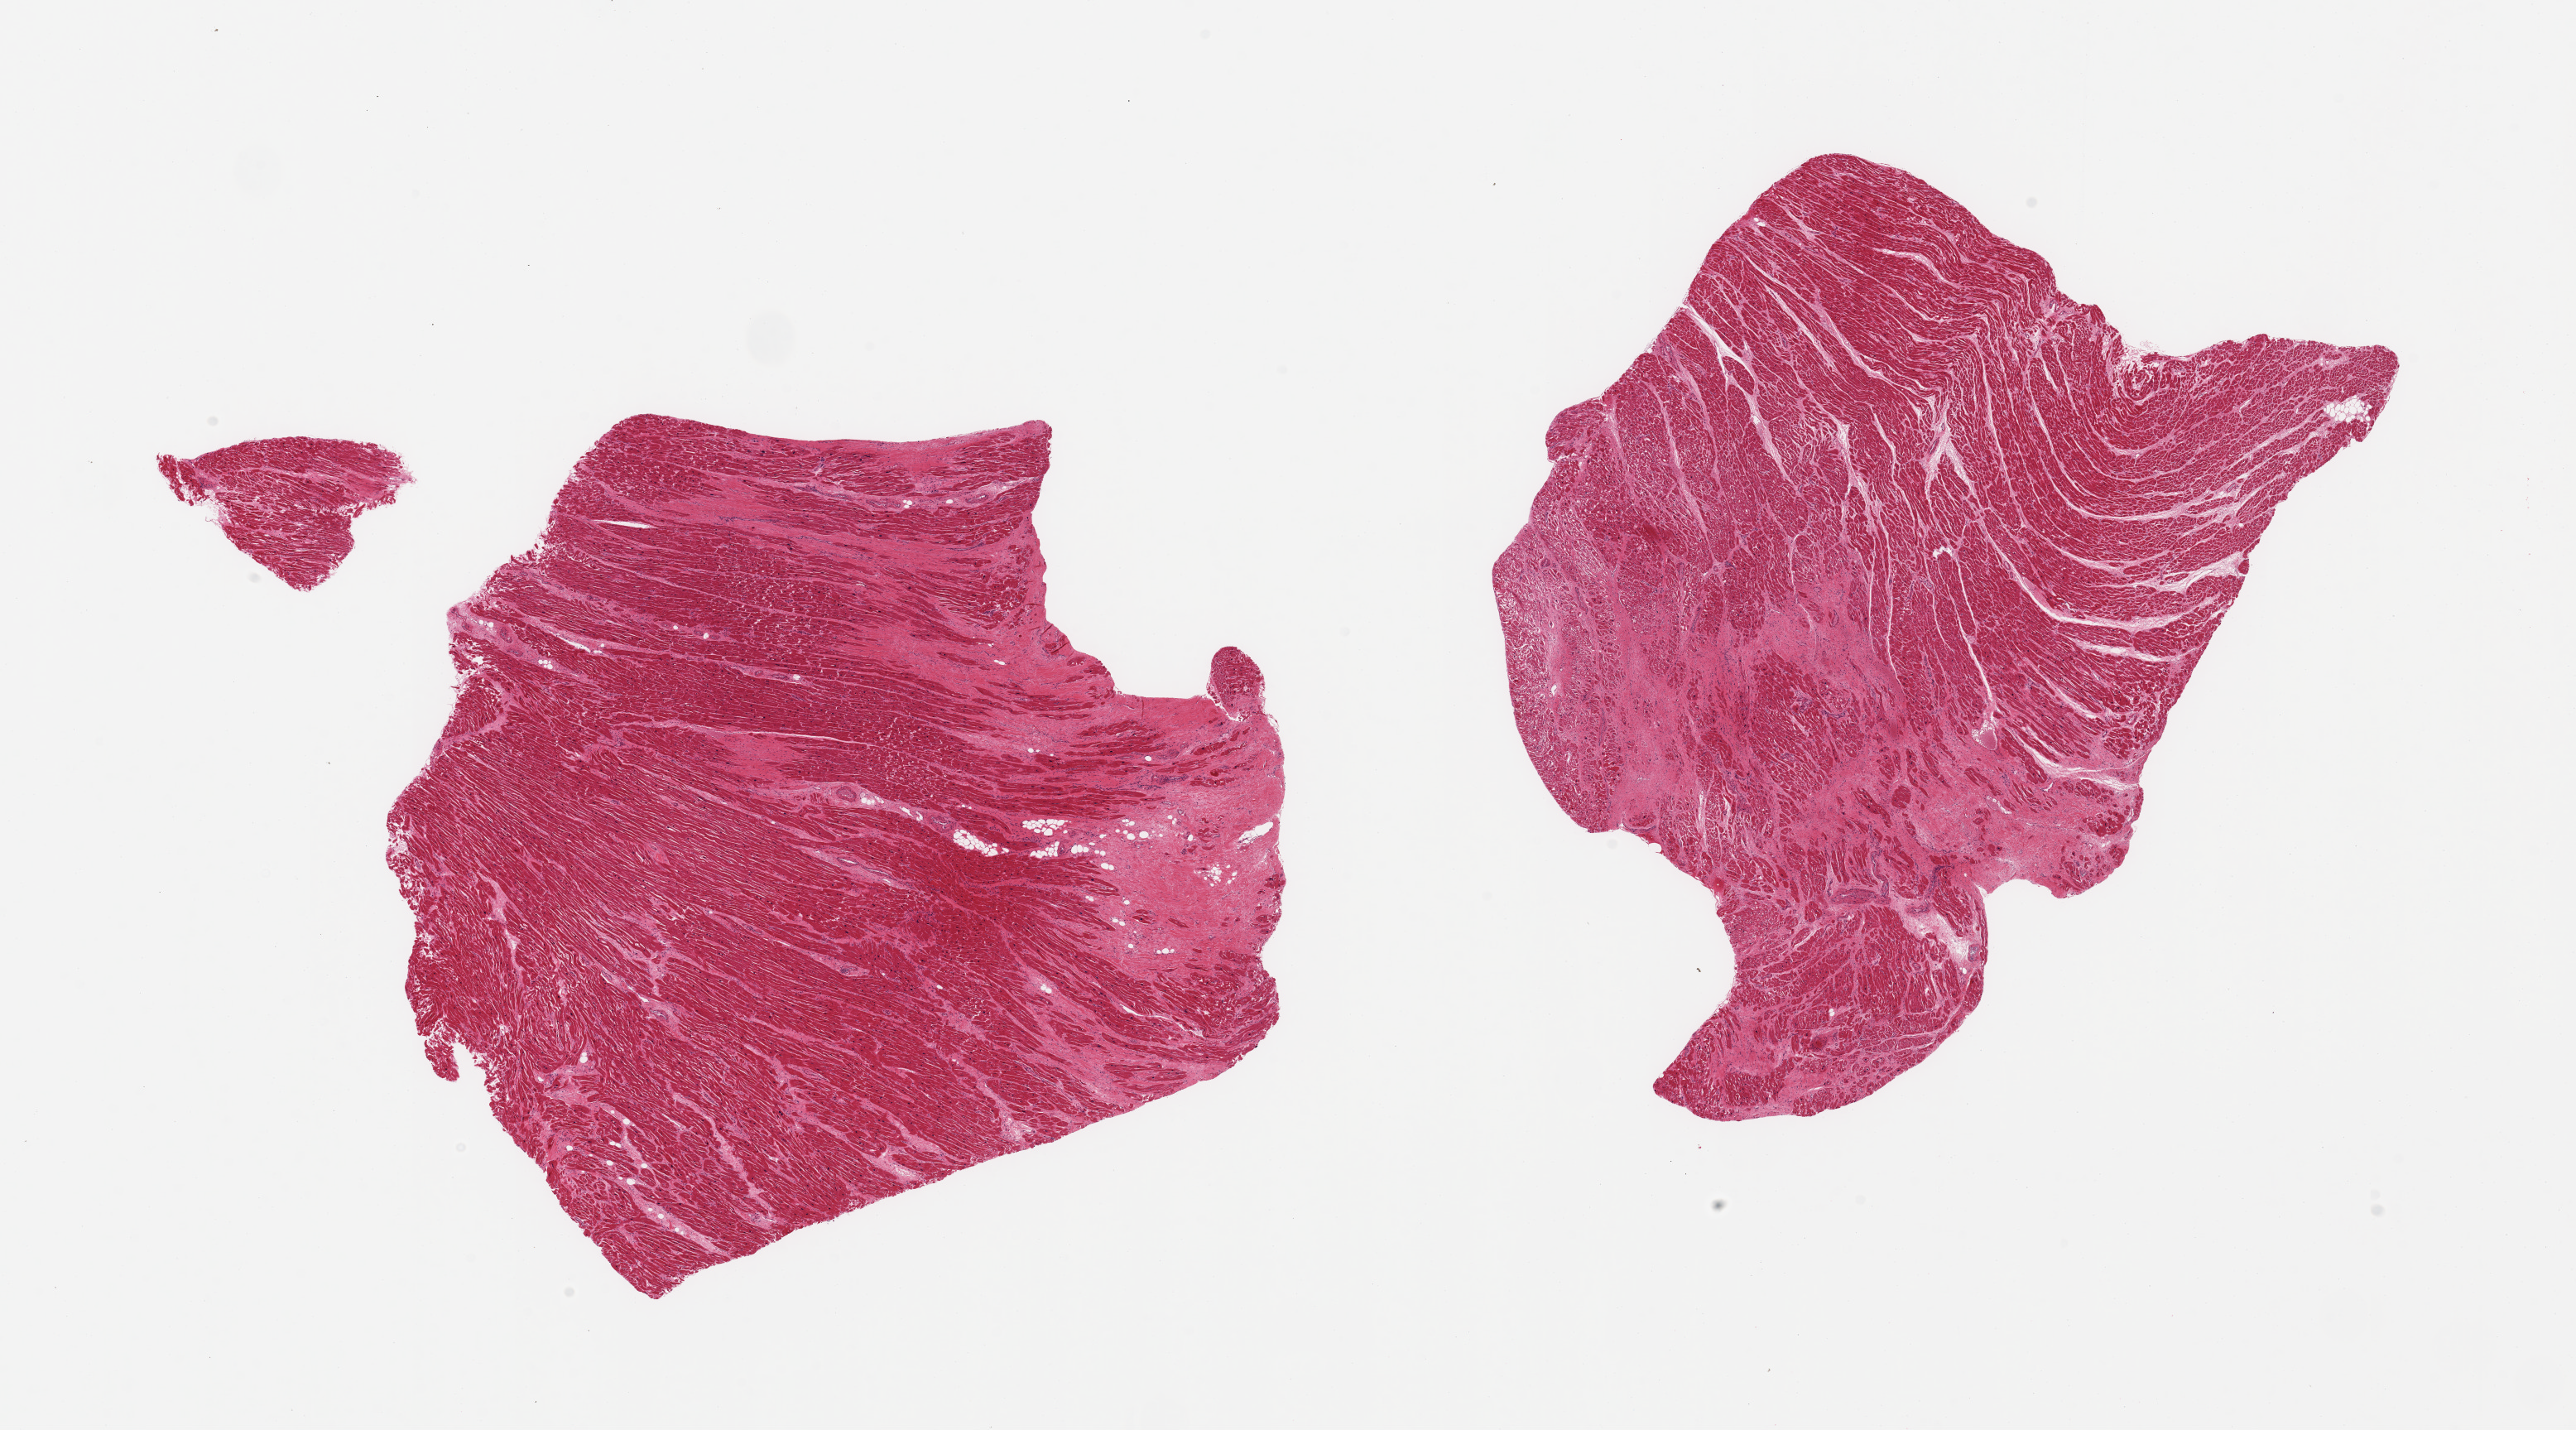
Whole-slide image, hematoxylin and eosin (H&E) stain, a low-resolution overview of the entire scanned area, about 24.6 x 13.7 mm; PAXgene-fixed, paraffin-embedded tissue; target tissue: heart; donor tissue sample.
- reviewer comment on this tissue sample: 2 pieces, mulitfocal remote infarcts, up to ~5mm